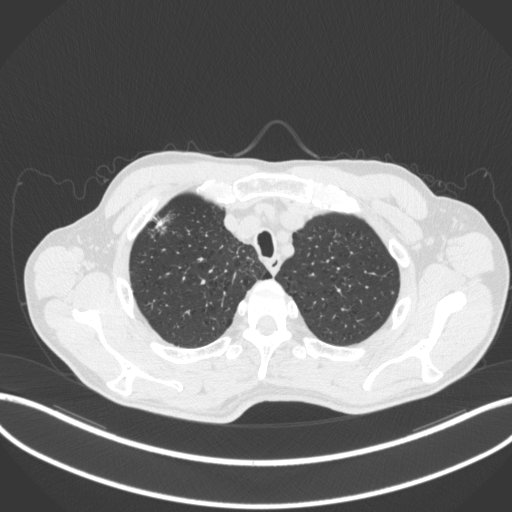
Chest CT, one axial slice; position 362 of 414 along the scan axis; lung window (W 1500 / L -600 HU); 1 mm slice thickness; 512 × 512 image matrix. Male patient, age 69 years. From the clinical record (not read from this slice): clinical TNM (as recorded): T1b N1 M0.
Structures marked on this image (rectangle marked by the reading radiologist):
- lung tumour (recorded histology: adenocarcinoma): bounding box [x1, y1, x2, y2] px = [151, 211, 173, 237]